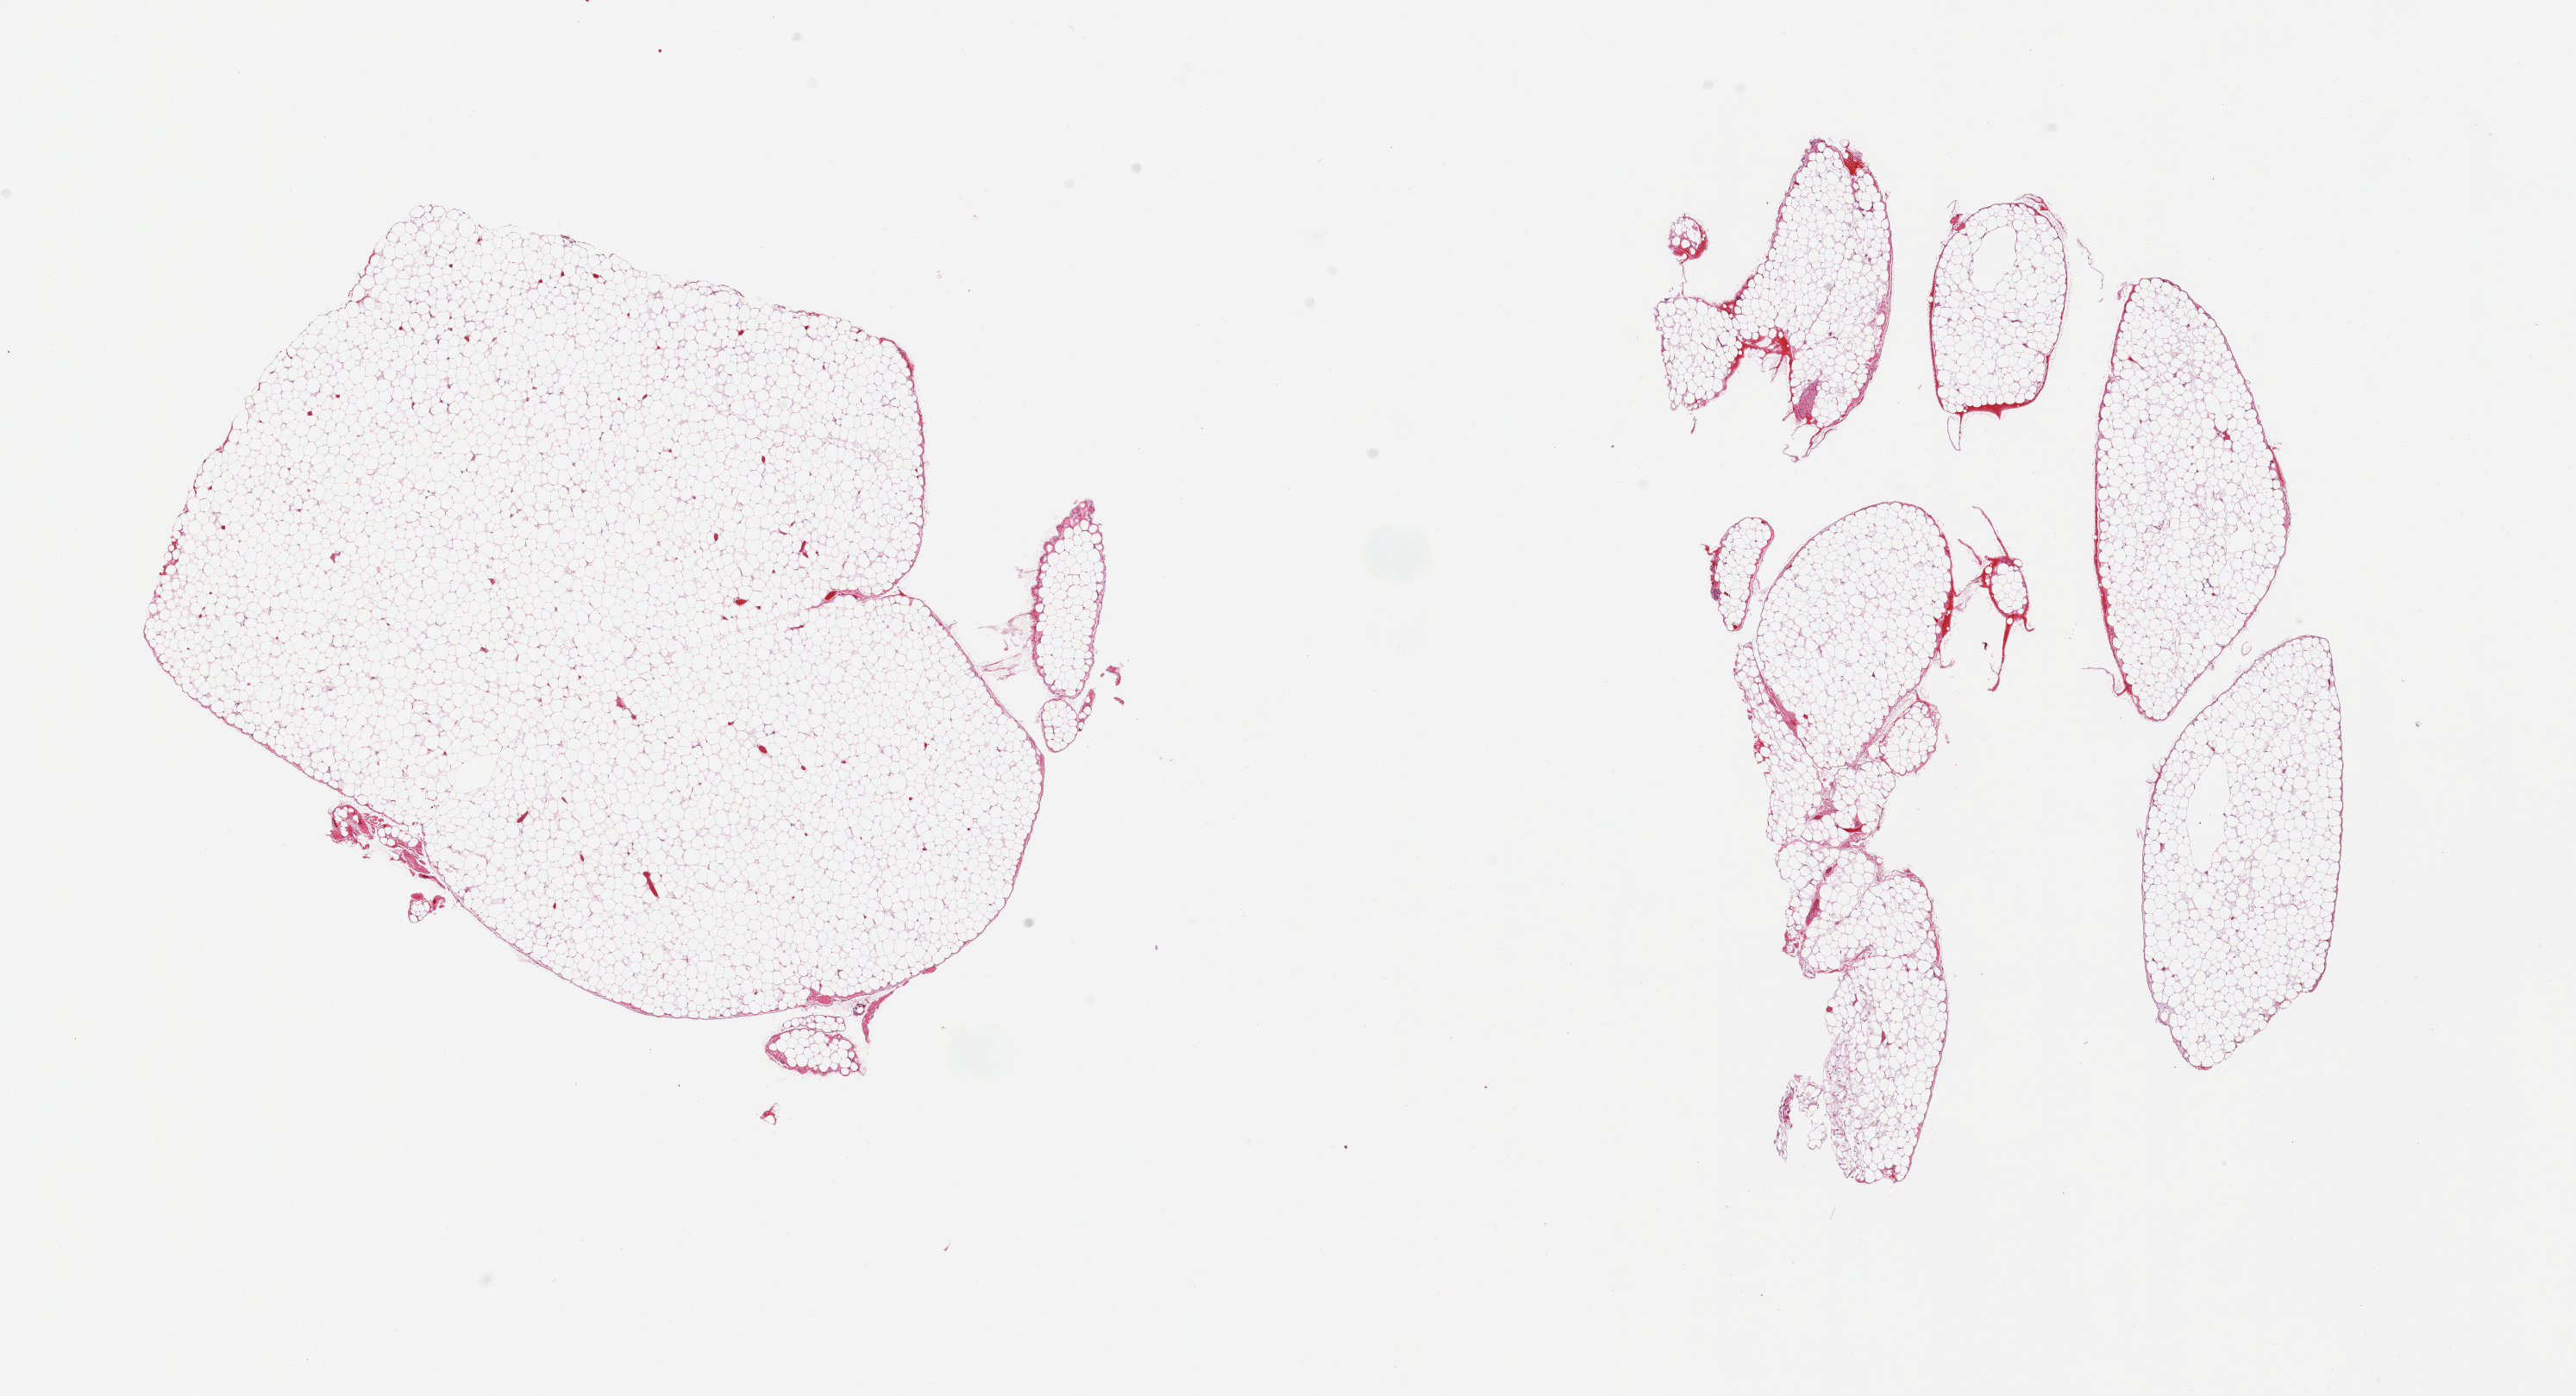
Digitized hematoxylin and eosin (H&E)-stained section, a low-resolution overview of the entire scanned area, about 23.6 x 12.8 mm. PAXgene-fixed paraffin-embedded (PFPE) section. Sampled site (target tissue): omentum. Donor tissue sample. Donor: male.
Reviewer comment on this tissue sample: 2 pieces.